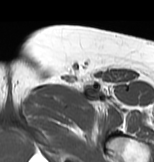
MRI of an extremity soft-tissue mass, one axial slice. Position 52 of 83 along the scan axis. MR volume resampled by the dataset authors to the PET/CT grid (not the native acquisition matrix). 3.27 mm slice thickness. 154 × 162 image matrix, field of view 150 × 158 mm. Female patient. From the clinical record (not read from this slice): histological type: myxofibrosarcoma; grade: intermediate; site of the primary tumour: left thigh.
Structures marked on this image (expert contour drawn on MRI and transferred to this co-registered scan by the dataset authors):
- gross tumour volume including surrounding oedema: bounding box [x1, y1, x2, y2] px = [30, 83, 118, 117]